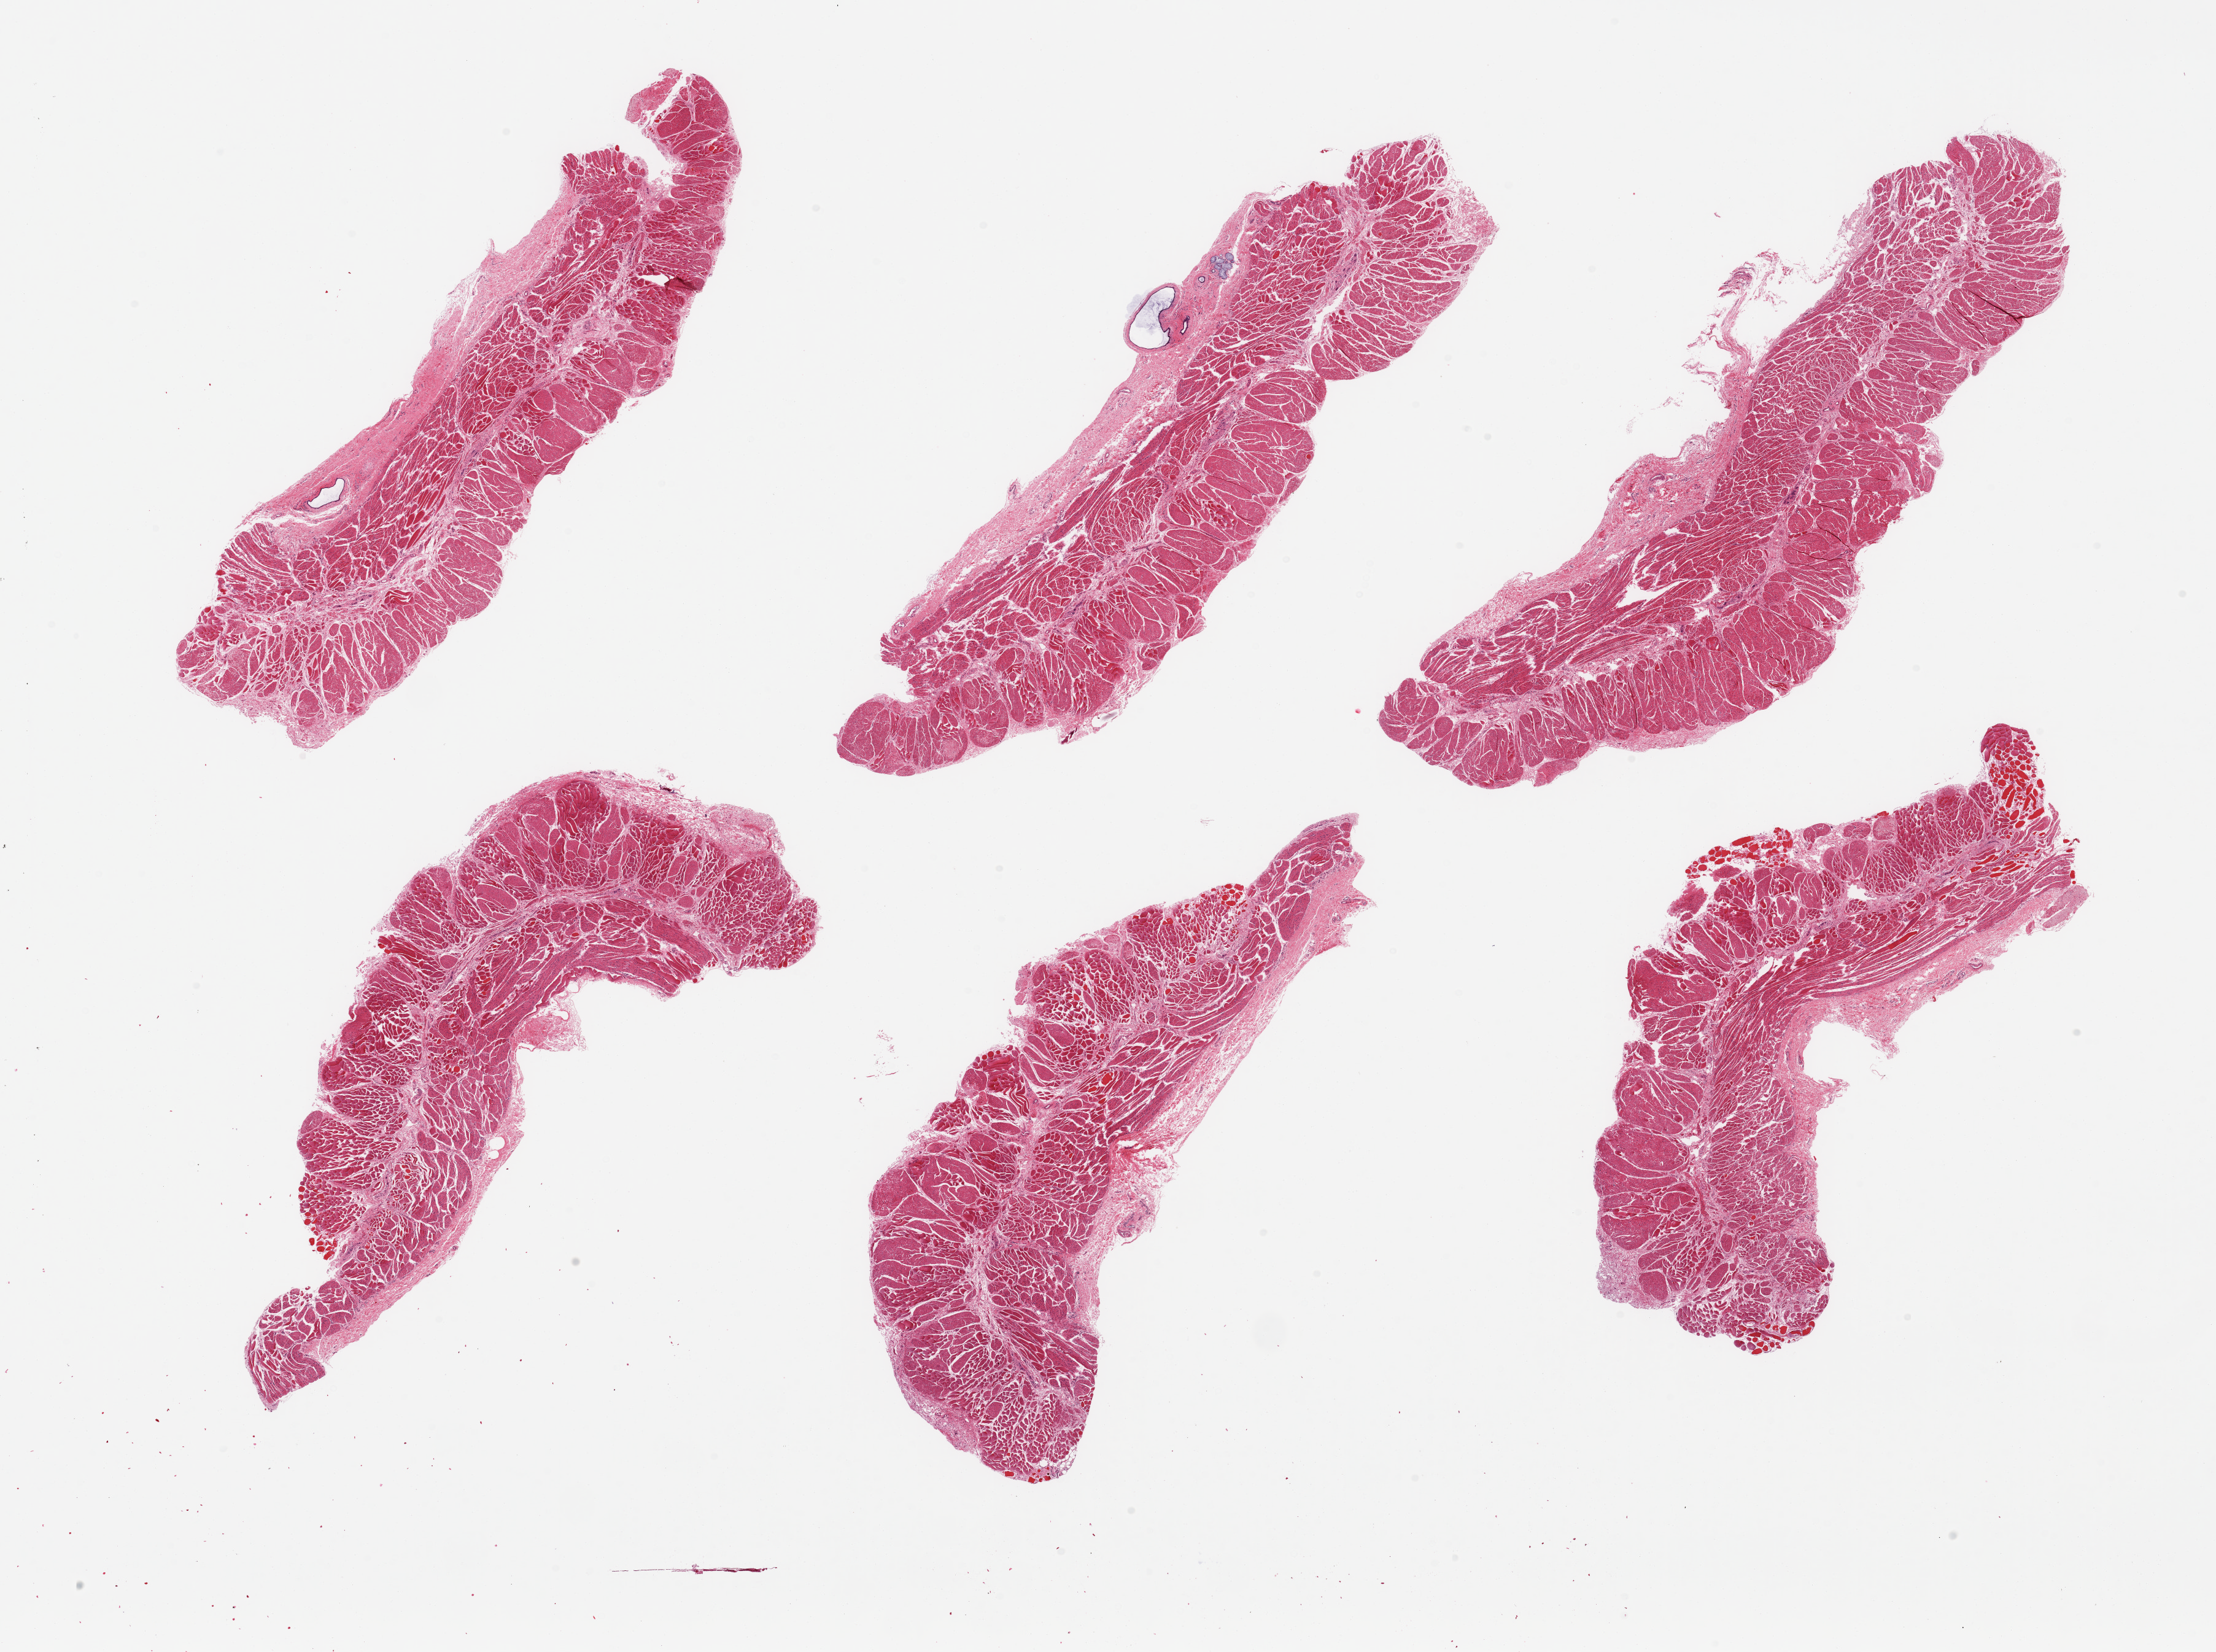
Whole-slide image, H&E stain — a low-resolution overview of the entire scanned area, about 28.5 x 21.3 mm (acquisition: 20x scan), PAXgene-fixed paraffin-embedded (PFPE) section, target tissue: esophageal muscle, donor tissue sample. Female donor.
Reviewer comment on this tissue sample: 6 pieces, confirmed target muscularis.